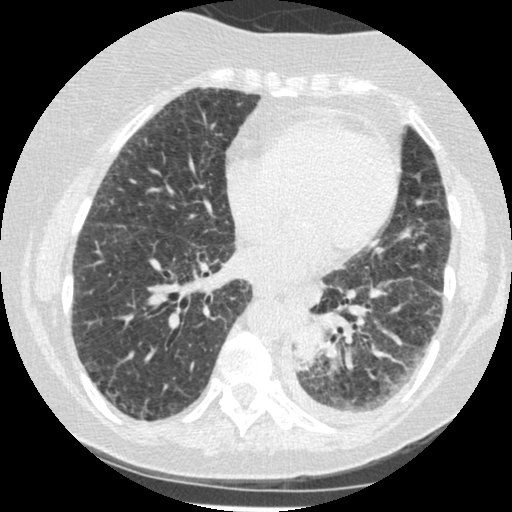
Low-dose screening chest CT, one axial slice. Position 83 of 341 along the scan axis. Reconstruction kernel STANDARD. Lung window (W 1500 / L -600 HU). 1.25 mm slice thickness. 512 × 512 image matrix.
Outlined on this slice (manually delineated by an expert):
- lesion 1 (tumor, lower lobe of left lung): bounding box <291,321,322,371> (left, top, right, bottom; pixels)